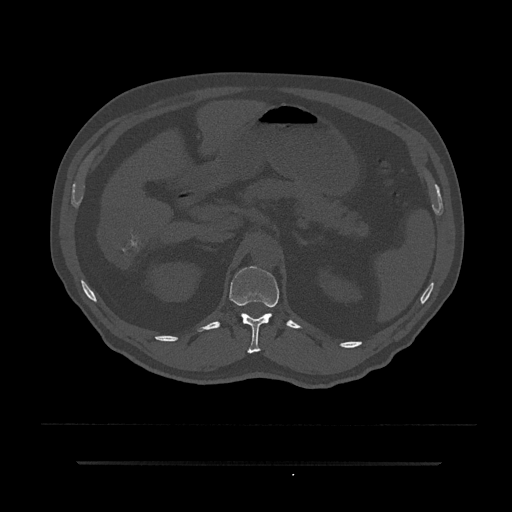
CT including the spine, one axial slice; position 200 of 797 along the scan axis; 120 kVp; bone window (W 1800 / L 400 HU); 0.5 mm slice thickness; 512 × 512 image matrix, field of view 464 × 464 mm. Male patient, age 59 years. From the clinical record (not read from this slice): primary cancer: bile ducts; vertebrae with lytic lesions (as recorded): T10.
Annotated regions visible in this slice (semi-automatically segmented with operator editing):
- T12 vertebra: box from (x=229, y=266) to (x=279, y=354) px